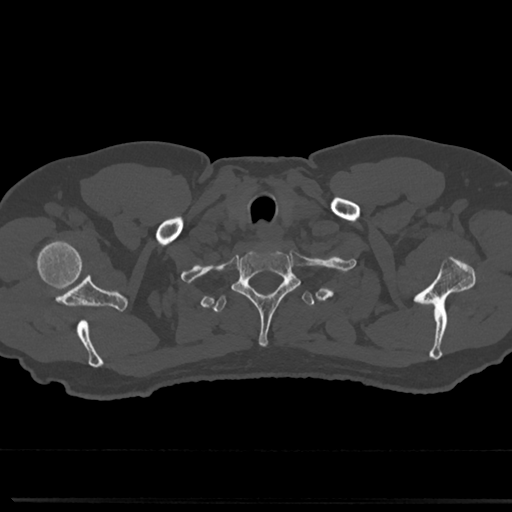
CT including the spine, one axial slice. Position 668 of 817 along the scan axis. 120 kVp. Bone window (W 1800 / L 400 HU). 512 × 512 image matrix, field of view 355 × 355 mm. Patient: male, 61 years. Case-level facts recorded for this patient, not image findings: primary cancer: prostate.
Structures marked on this image (semi-automatically segmented with operator editing):
- T1 vertebra: bounding box (x1, y1, x2, y2) in pixels: (233, 247, 298, 344)
- T2 vertebra: (212, 278, 315, 315)